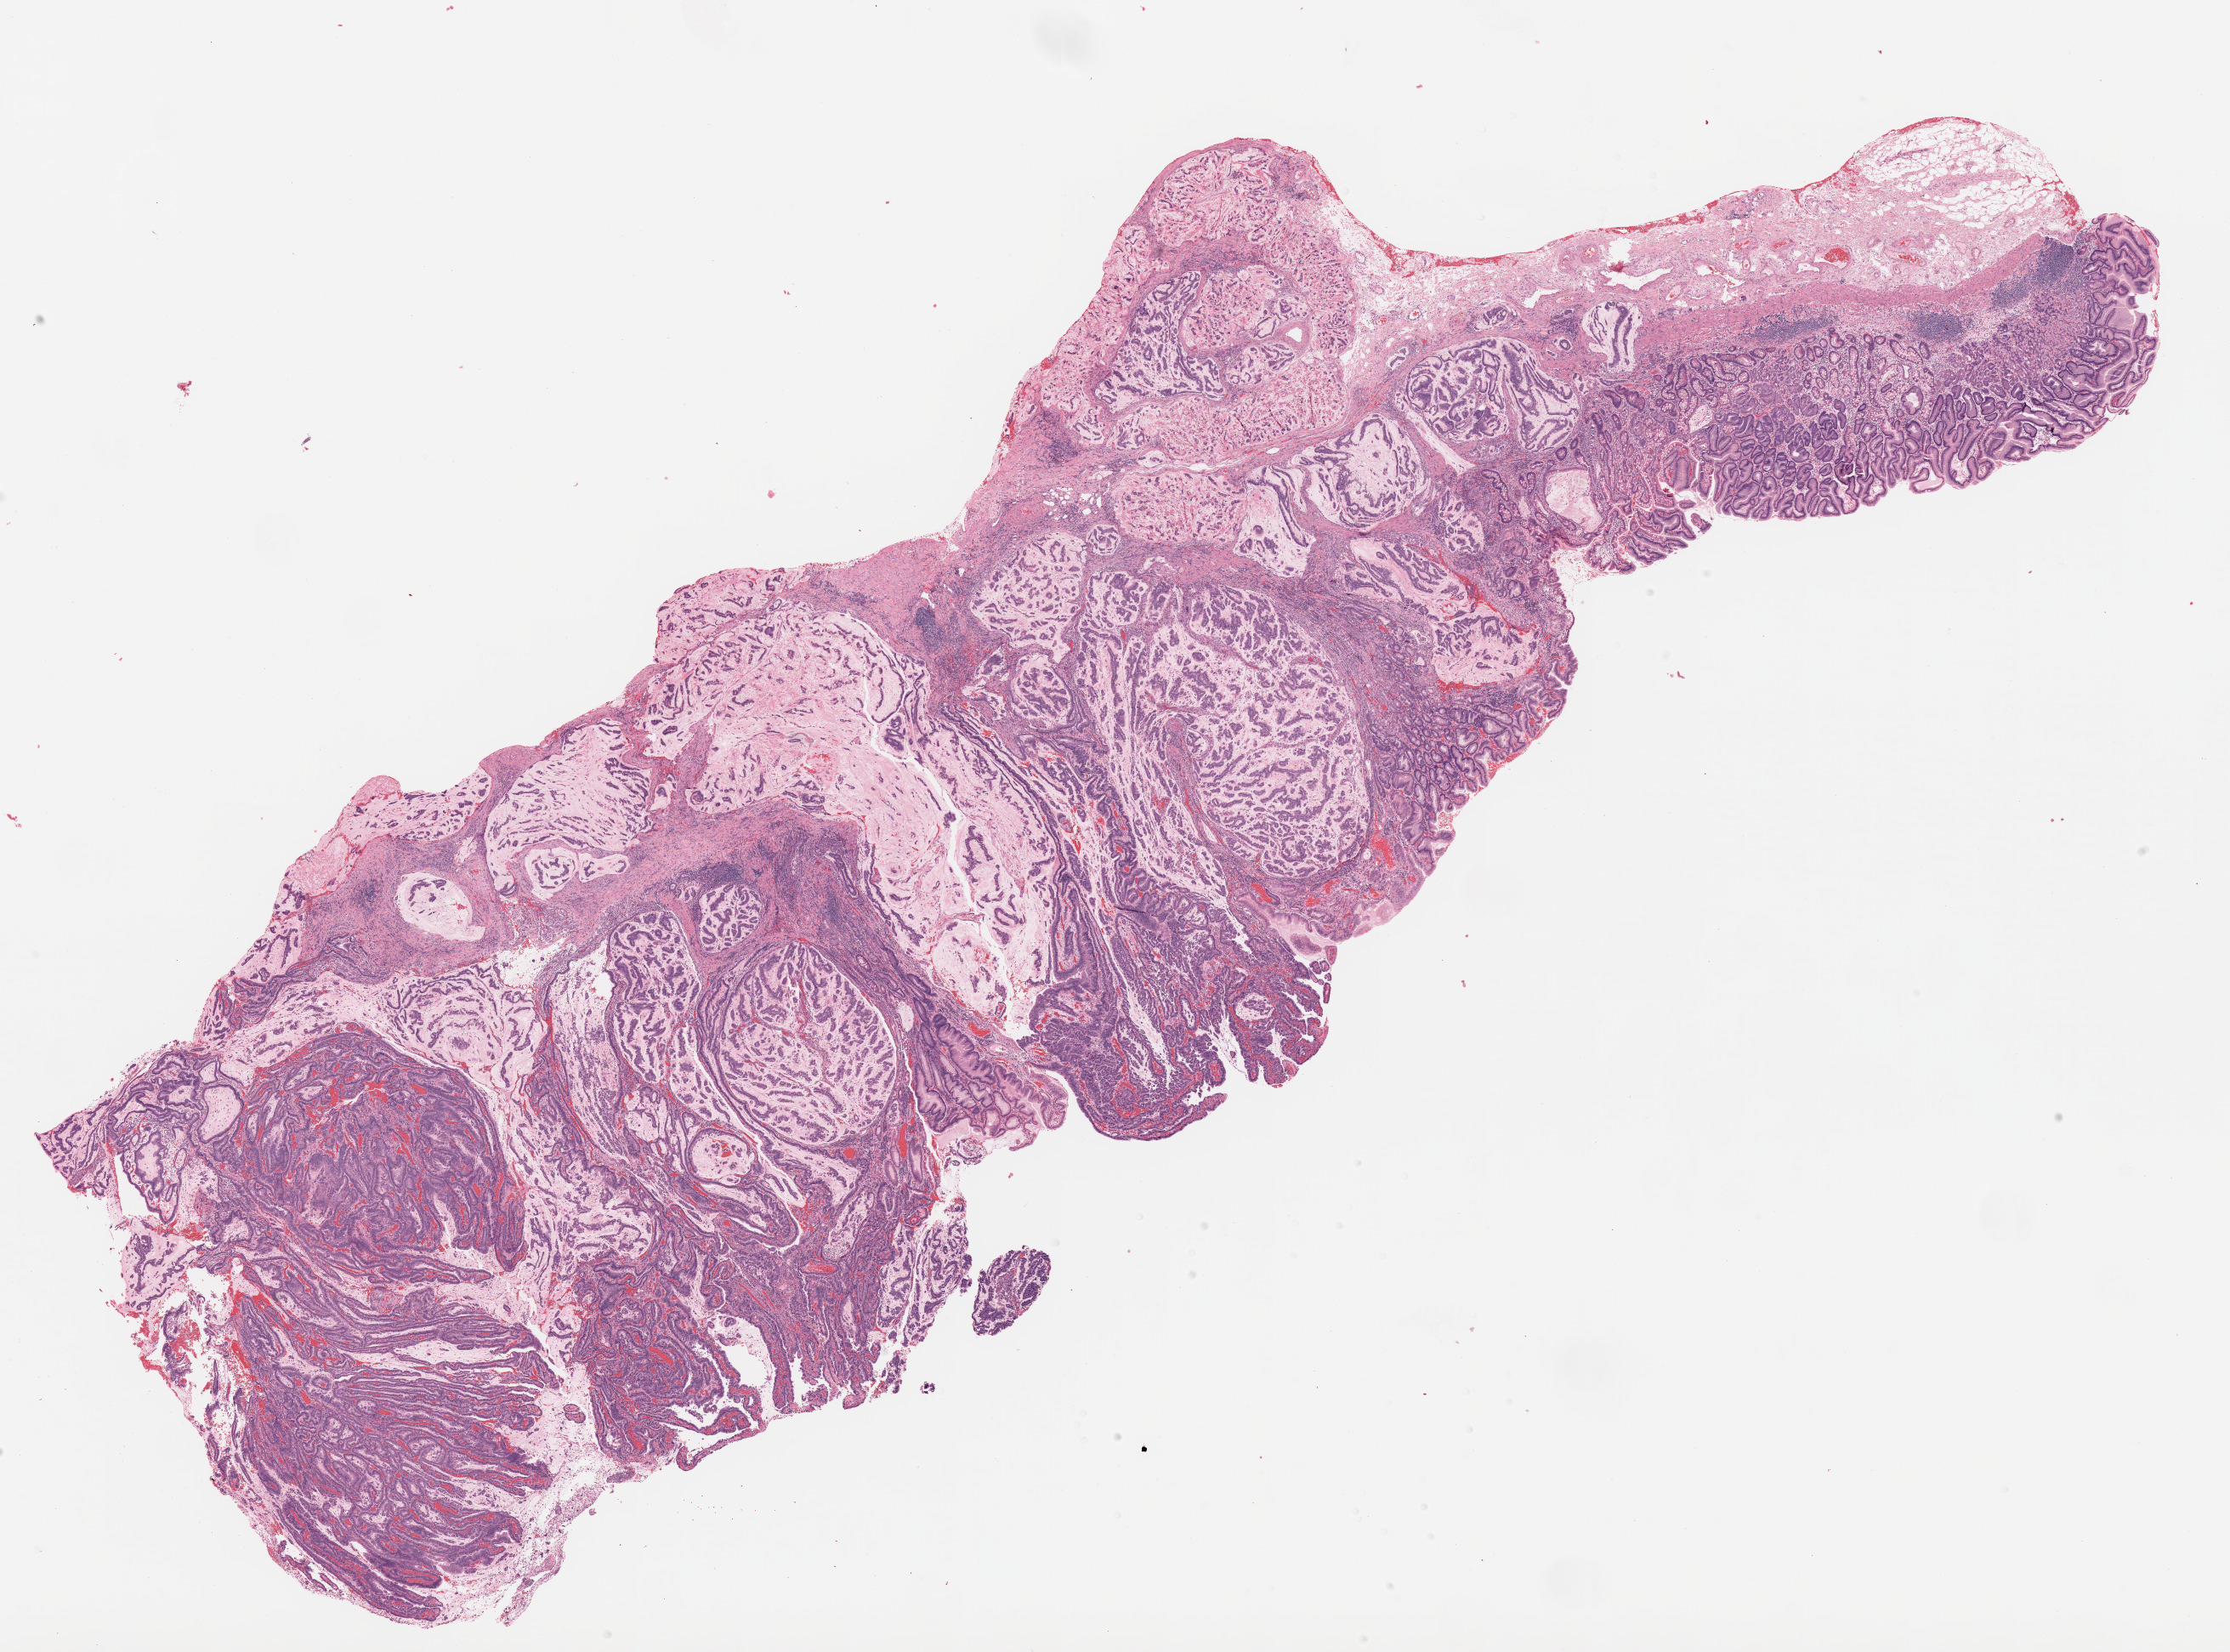
H&E whole-slide image — a low-resolution overview of the entire scanned area, about 21.0 x 15.6 mm (from a 20x scan), FFPE section, stomach, primary tumour sample. Female patient. Histologic grade: G2 (moderately differentiated).
- AJCC pathologic stage: IV (6th edition)
- lymph nodes positive (case pathology): 16 of 53 examined
- histologic diagnosis: Mucinous adenocarcinoma